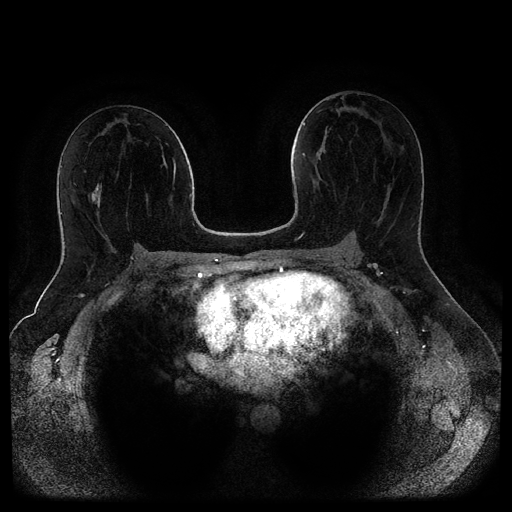
Breast MRI (dynamic contrast-enhanced, multi-phase), one axial slice; slice 52 of 116 in the series (ordered by position); dynamic contrast-enhanced series, time point 2 of 5 at this slice position (early post-contrast); 1.5 T; TE 2.6 ms, TR 5.3 ms; 512 × 512 image matrix, field of view 370 × 370 mm. Patient: female, 44 years.
Annotated regions visible in this slice (semi-automatic segmentation, software-assisted and operator-edited):
- breast lesion (labelled benign in the annotation): bounding box (x1, y1, x2, y2) in pixels: (89, 184, 102, 208)